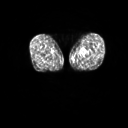
FDG PET of an extremity soft-tissue mass (from a PET/CT study), one axial slice. Slice 6 of 267 in the series (ordered by position). 128 × 128 image matrix, field of view 600 × 600 mm. Male patient, age 59 years. From the clinical record (not read from this slice): histological type: pleiomorphic liposarcoma; grade: high; site of the primary tumour: left thigh.
Outlined on this slice (expert contour drawn on MRI and transferred to this co-registered scan by the dataset authors):
- gross tumour volume including surrounding oedema: box from (x=79, y=52) to (x=87, y=58) px